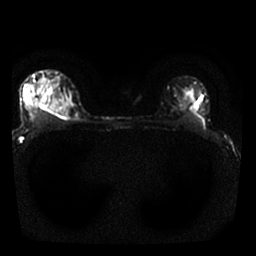
Breast MRI, one axial slice; position 20 of 25 along the scan axis; diffusion-weighted series; image 2 of 4 stored at this slice position (different b-values; order by instance number); 1.5 T; 256 × 256 image matrix, field of view 310 × 310 mm. Female patient.
Outlined on this slice (outlined manually by an expert reader):
- tumour on diffusion-weighted imaging: bounding box (x1, y1, x2, y2) in pixels: (40, 98, 67, 117)